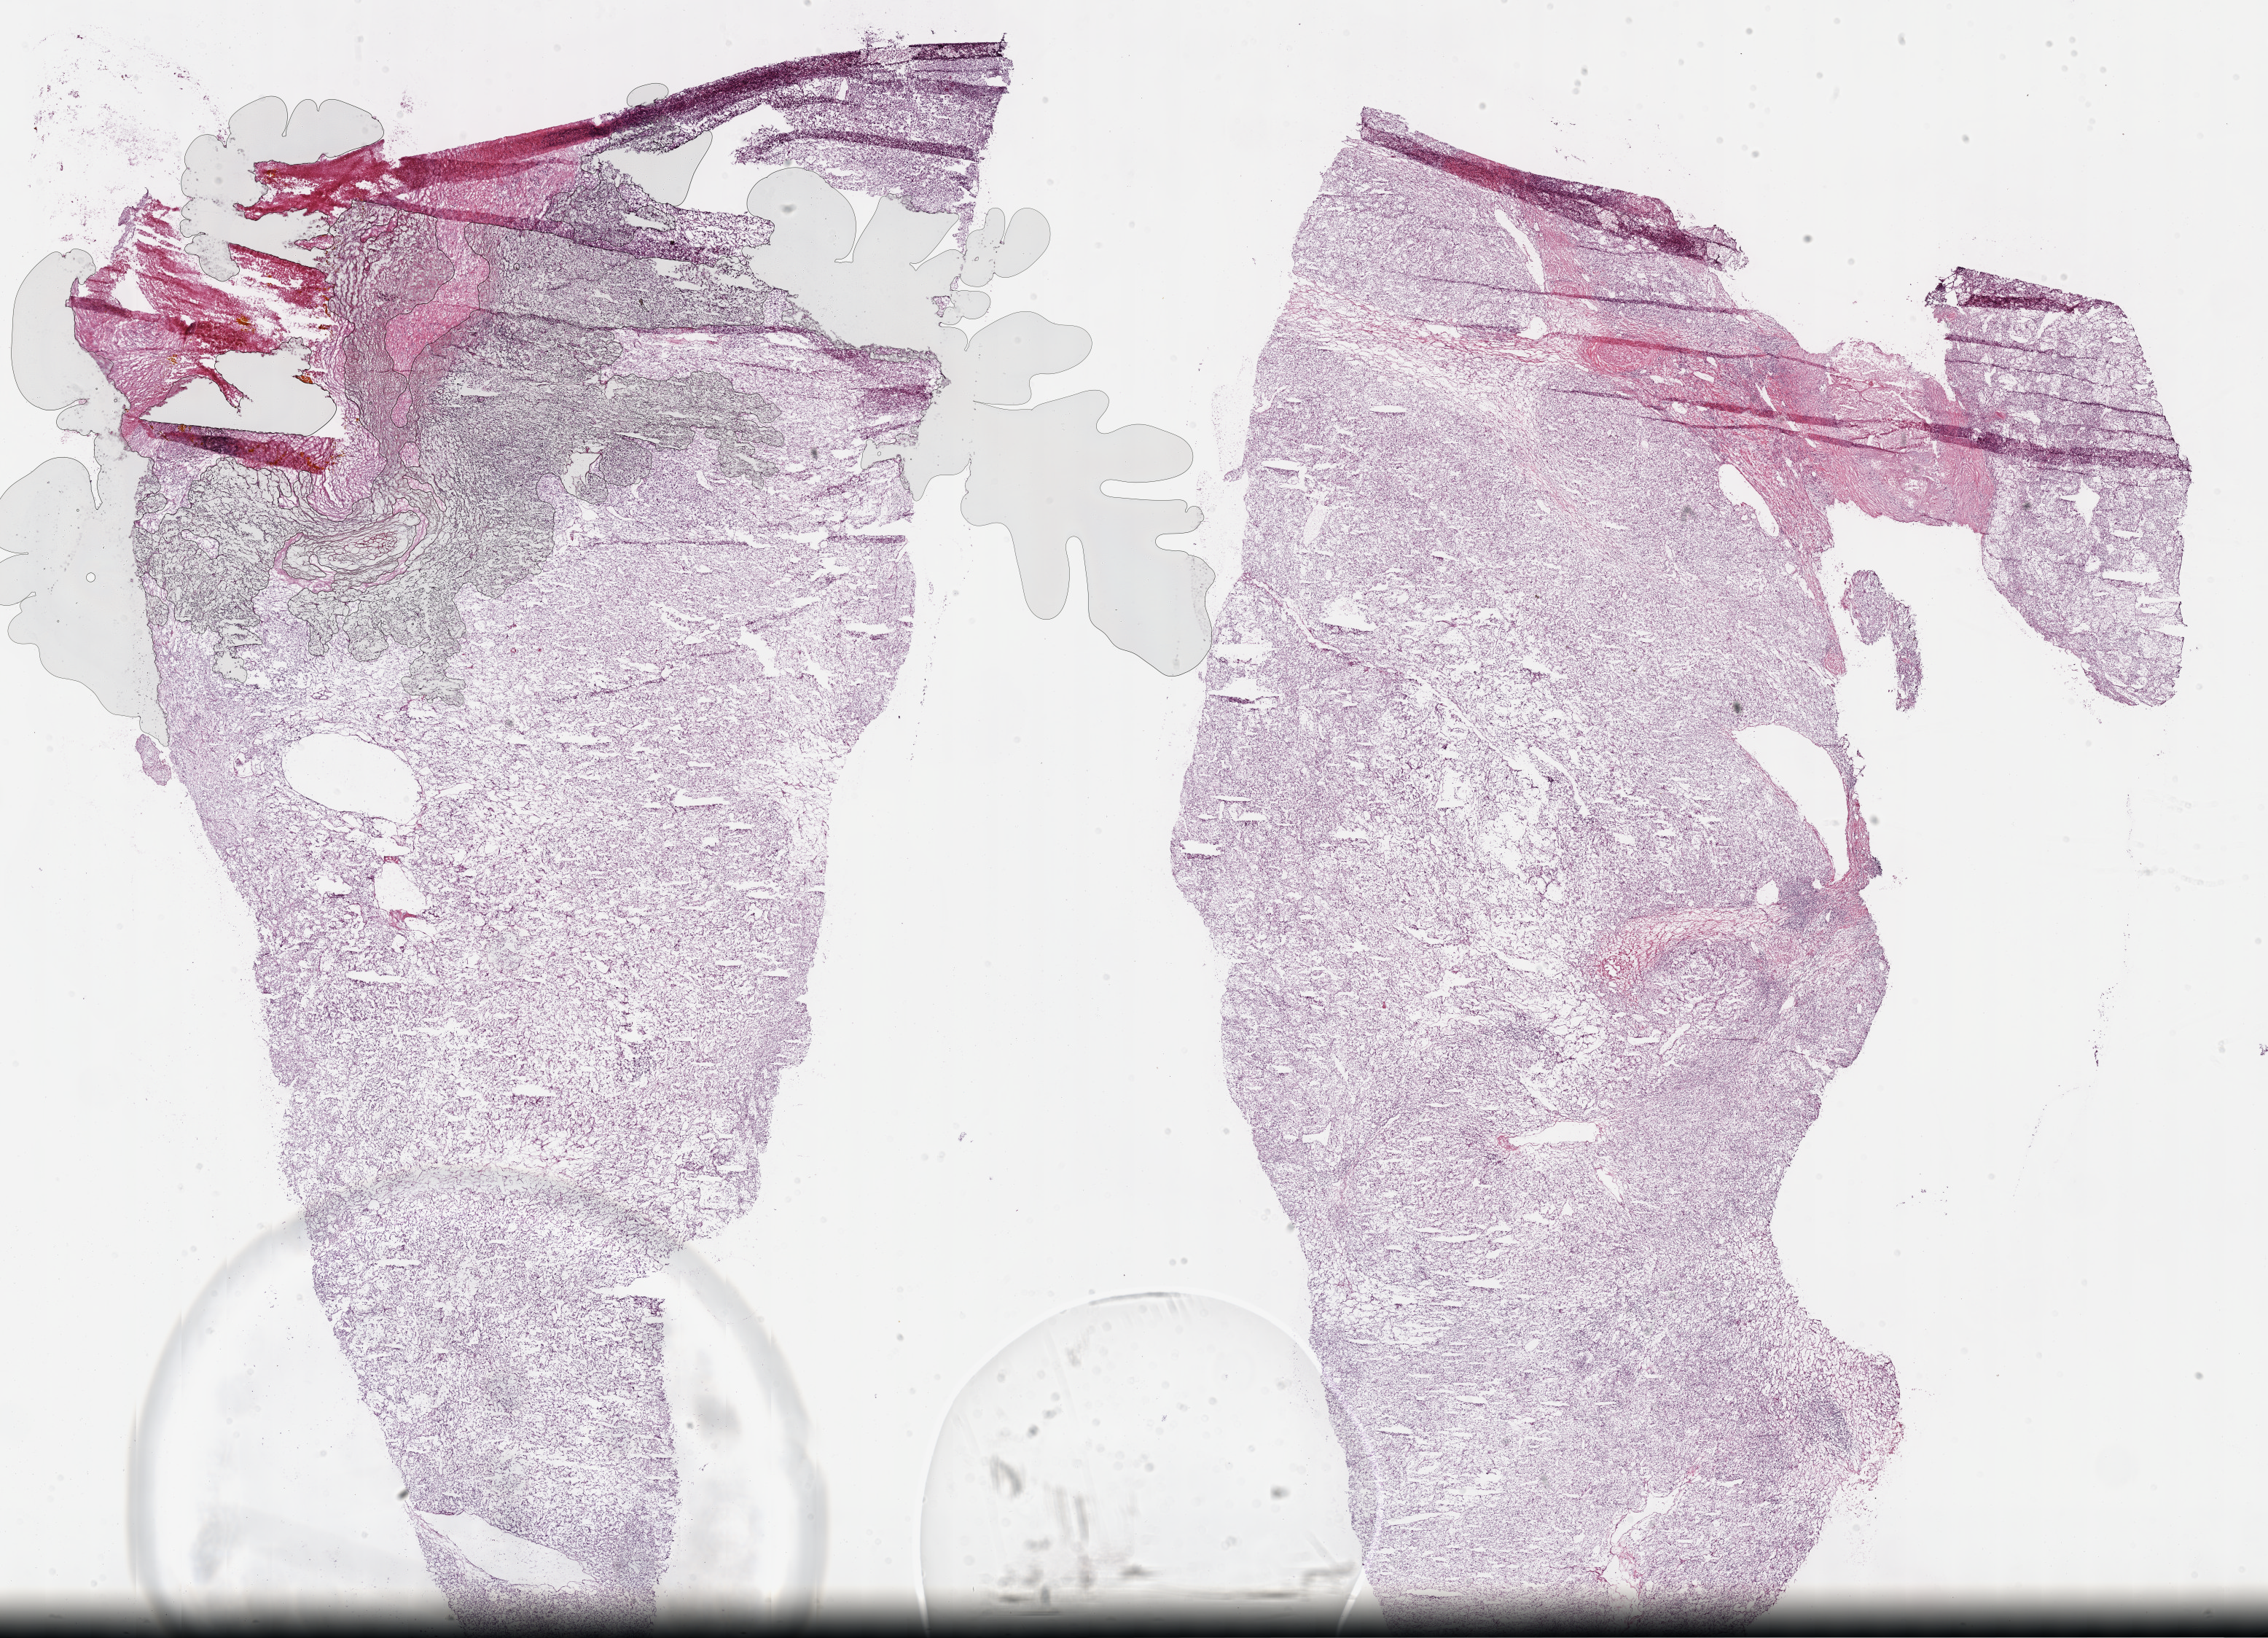
H&E-stained whole-slide image — whole scanned area (about 25.2 x 18.2 mm, from a 40x scan) shown as a low-resolution overview; frozen section; sample: primary tumour, kidney. Female, age 66 years at initial diagnosis. Histologic grade: G3 (poorly differentiated). Slide review estimates, as recorded: tumour cells 85%, tumour nuclei 85%, normal cells 0%, stromal cells 10%, necrosis 5%.
Lymph nodes positive (case pathology): 0 of 1 examined. AJCC pathologic stage: IV. Histologic diagnosis: Clear cell adenocarcinoma, NOS. Laterality: left.